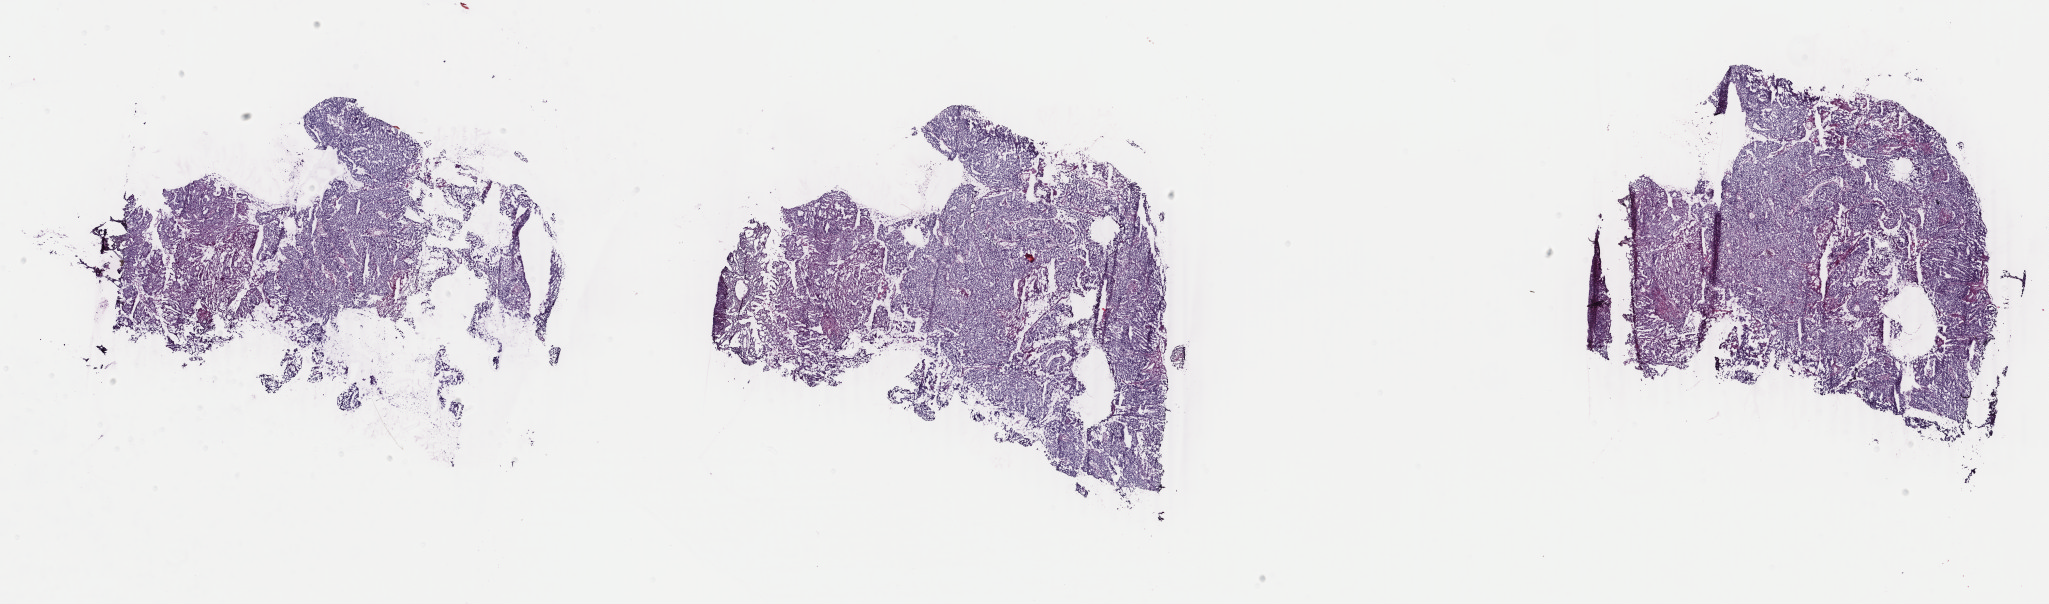
H&E-stained whole-slide image, low-resolution overview of the scanned area, about 32.6 x 9.6 mm; frozen section from the top of the tissue portion; uterus, primary tumour sample. Female patient; age at initial diagnosis 65 years. Histologic grade: G3 (poorly differentiated). Slide review estimates, as recorded: tumour cells 100%, tumour nuclei 90%, normal cells 0%, stromal cells 0%, necrosis 0%. Infiltration values recorded for this section: lymphocyte infiltration 0%, monocyte infiltration 0%, neutrophil infiltration 0%.
FIGO stage: IB. Pathologic diagnosis: Endometrioid adenocarcinoma, NOS (endometrium).